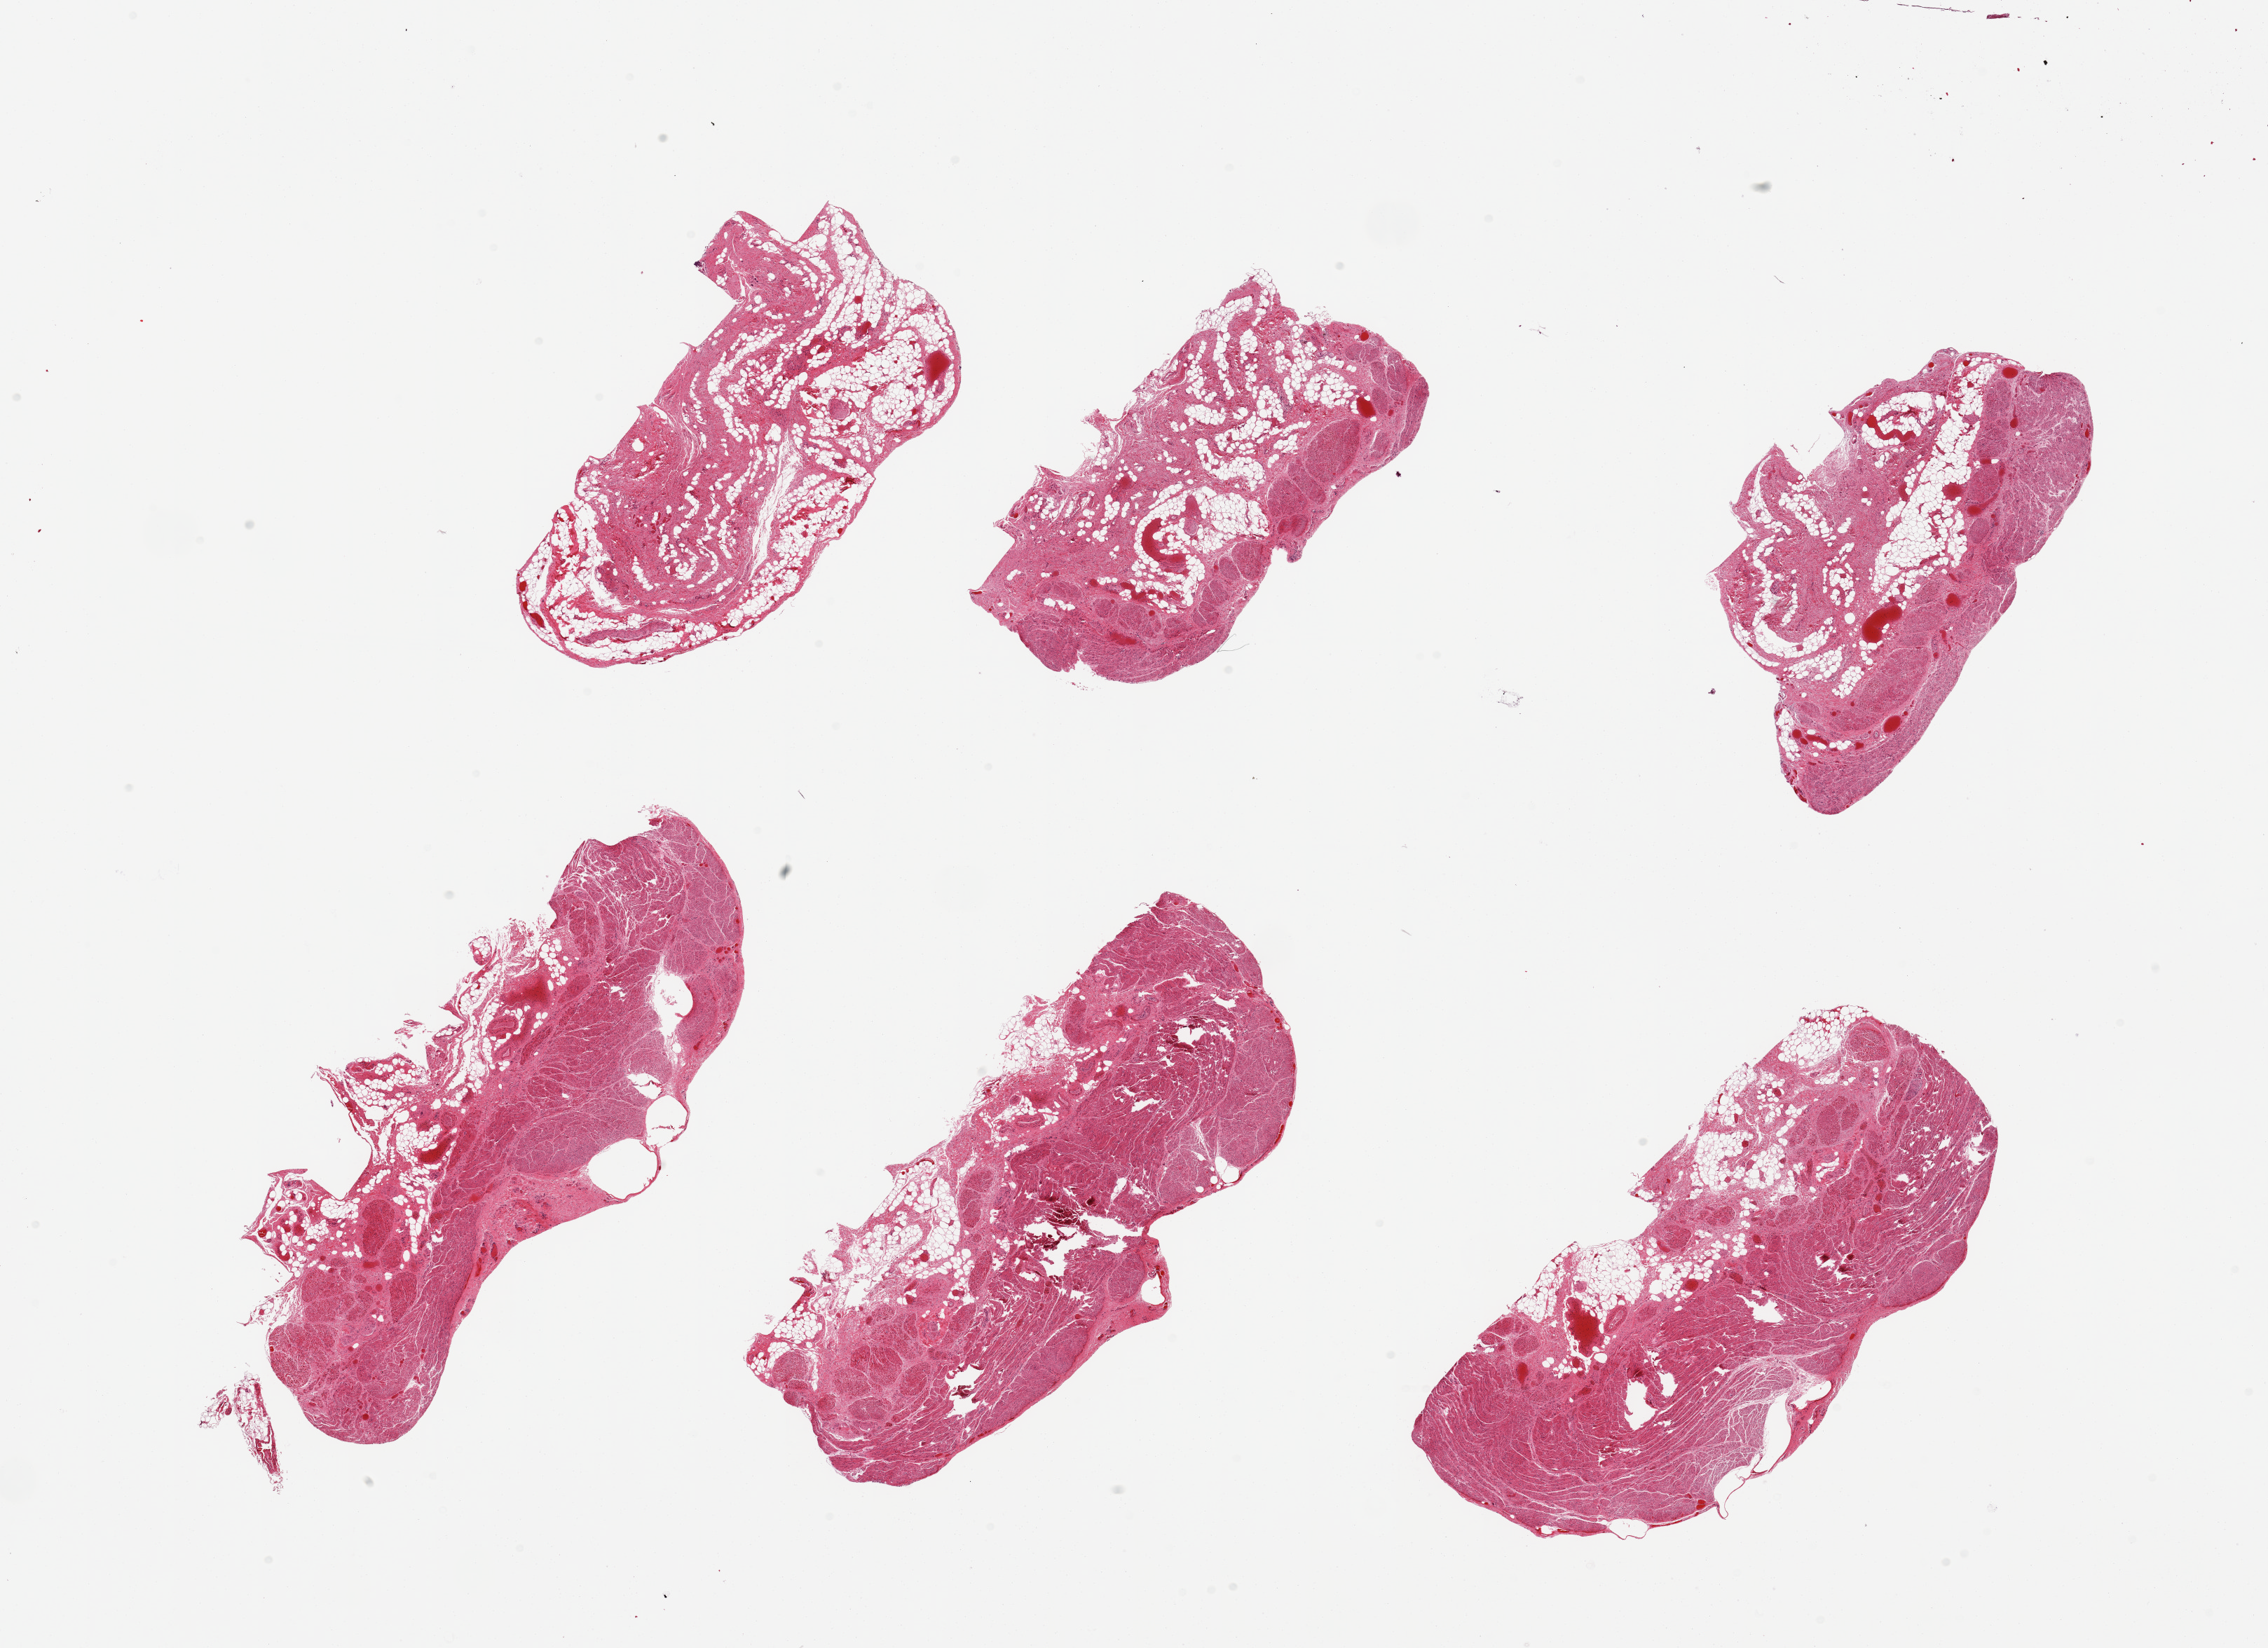
Whole-slide image, haematoxylin and eosin stain, brightfield — shown as a low-resolution overview of the whole scanned area (about 25.6 x 18.6 mm, slide scanned at 20x), PAXgene-fixed paraffin-embedded (PFPE) section, sampled site (target tissue): gastroesophageal junction, donor tissue sample. Donor: male.
Review note (as recorded): 6 pieces; excessive (30 to 100%) fibrofatty submucosa.